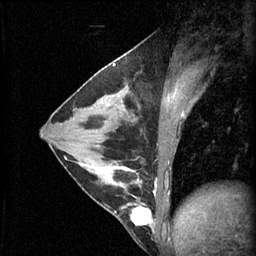
Breast MRI (dynamic contrast-enhanced), one sagittal slice; slice 28 of 60 in the series (ordered by position); 3 images stored at this slice position (order not interpretable as contrast timing); 1.5 T; TE 4.2 ms, TR 11 ms; 2.1 mm slice thickness; 256 × 256 image matrix, field of view 180 × 180 mm. Female patient, age 29 years.
Outlined on this slice (semi-automatic segmentation, software-assisted and operator-edited):
- analysis volume of interest (the breast-tissue region the enhancement analysis was run in; not a lesion): bounding box [x1, y1, x2, y2] px = [93, 164, 153, 229]
- tumour enhancement mask (voxels above the 70 % enhancement threshold inside the analysis volume of interest): [93, 166, 153, 227]